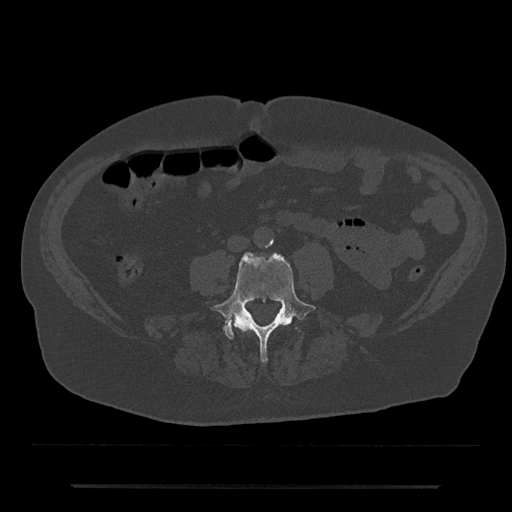
CT including the spine, one axial slice; slice 353 of 797 in the series (ordered by position); reconstruction kernel Br40s/3; bone window (W 1800 / L 400 HU); 0.5 mm slice thickness; 512 × 512 image matrix, field of view 434 × 434 mm. Patient: male, 80 years. From the clinical record (not read from this slice): primary cancer: prostate.
Annotated regions visible in this slice (semi-automatic segmentation, software-assisted and operator-edited):
- L4 vertebra: bounding box <210,252,316,363> (left, top, right, bottom; pixels)